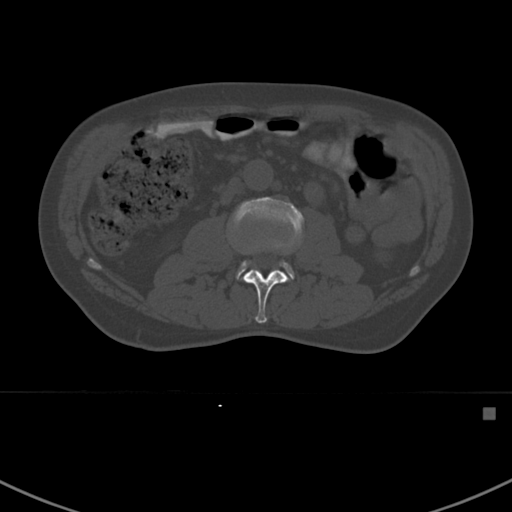
CT including the spine, one axial slice; slice 277 of 412 in the series (ordered by position); 120 kVp; bone window (W 1800 / L 400 HU); 512 × 512 image matrix, field of view 358 × 358 mm. Patient: male, 59 years. Case-level facts recorded for this patient, not image findings: primary cancer: prostate.
Outlined on this slice (semi-automatic segmentation, software-assisted and operator-edited):
- L2 vertebra: bounding box (x1, y1, x2, y2) in pixels: (242, 250, 289, 324)
- L3 vertebra: (229, 197, 304, 280)